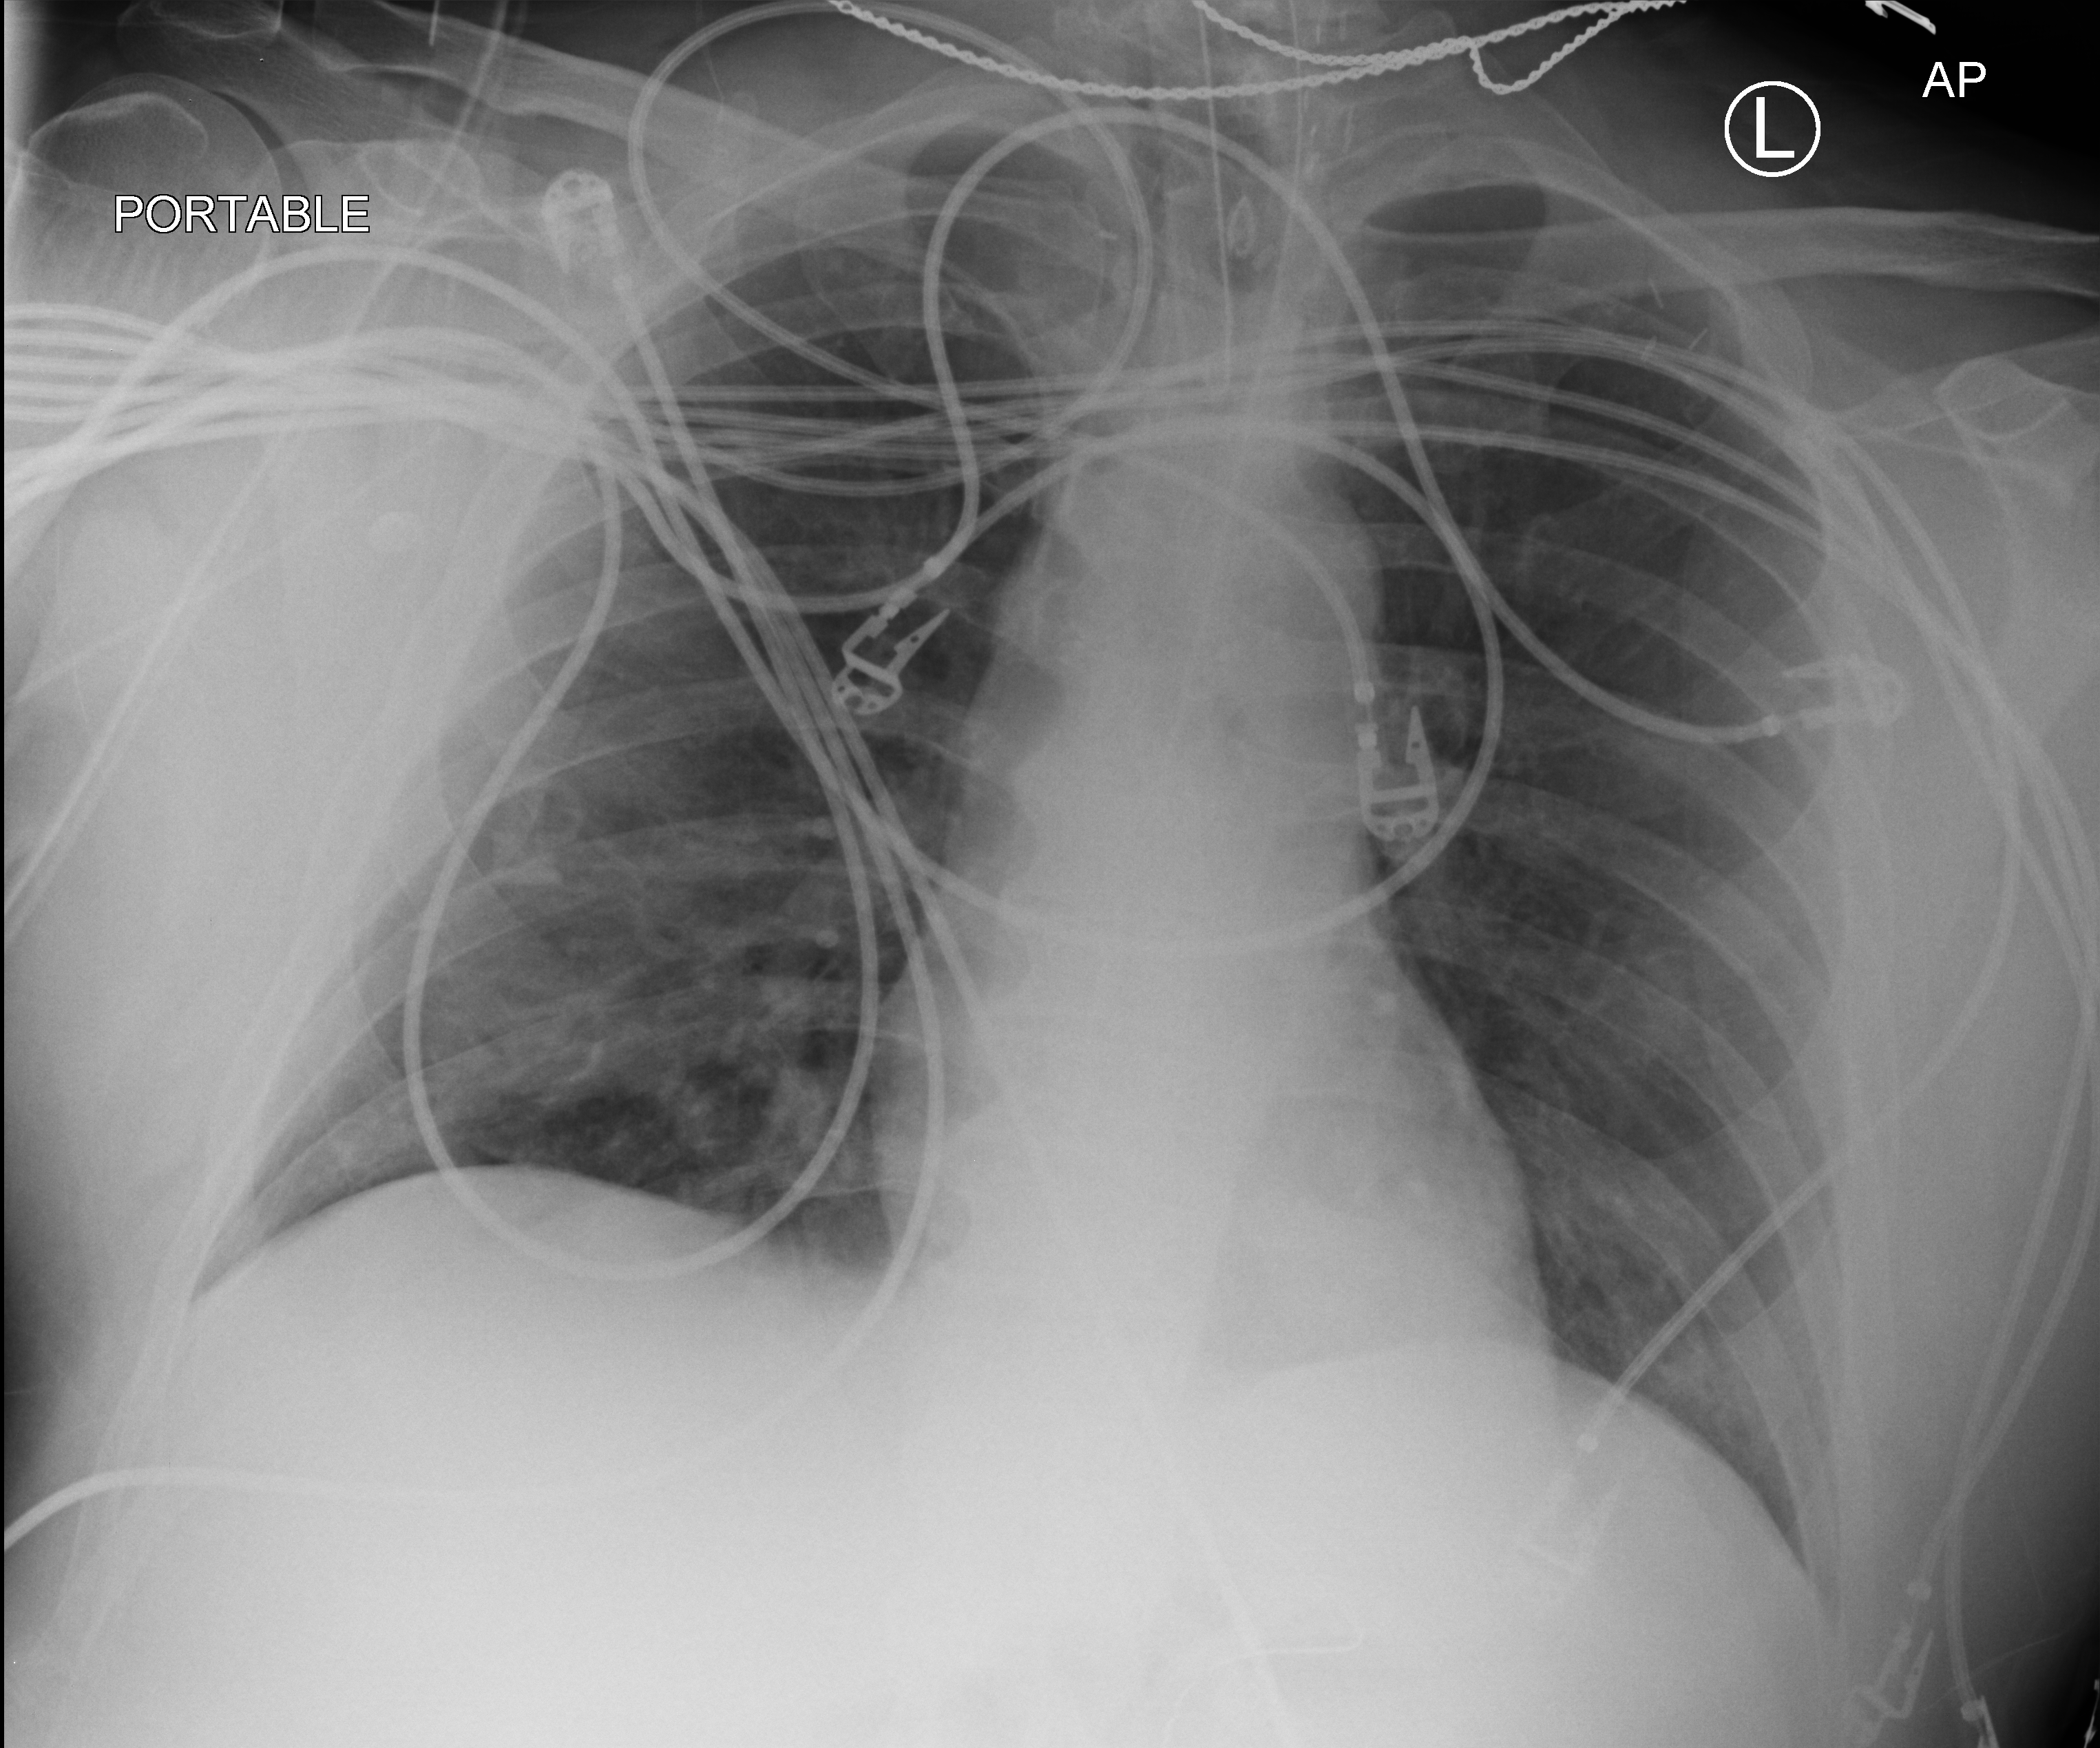
Bedside chest radiograph (computed radiography), anteroposterior (AP) projection. Patient hospitalised with COVID-19, aged 18–59 years.
Admission-level facts for this patient (not findings on this image; timing relative to this image not recorded): COPD (admission record): no; length of hospital stay: 19 days.